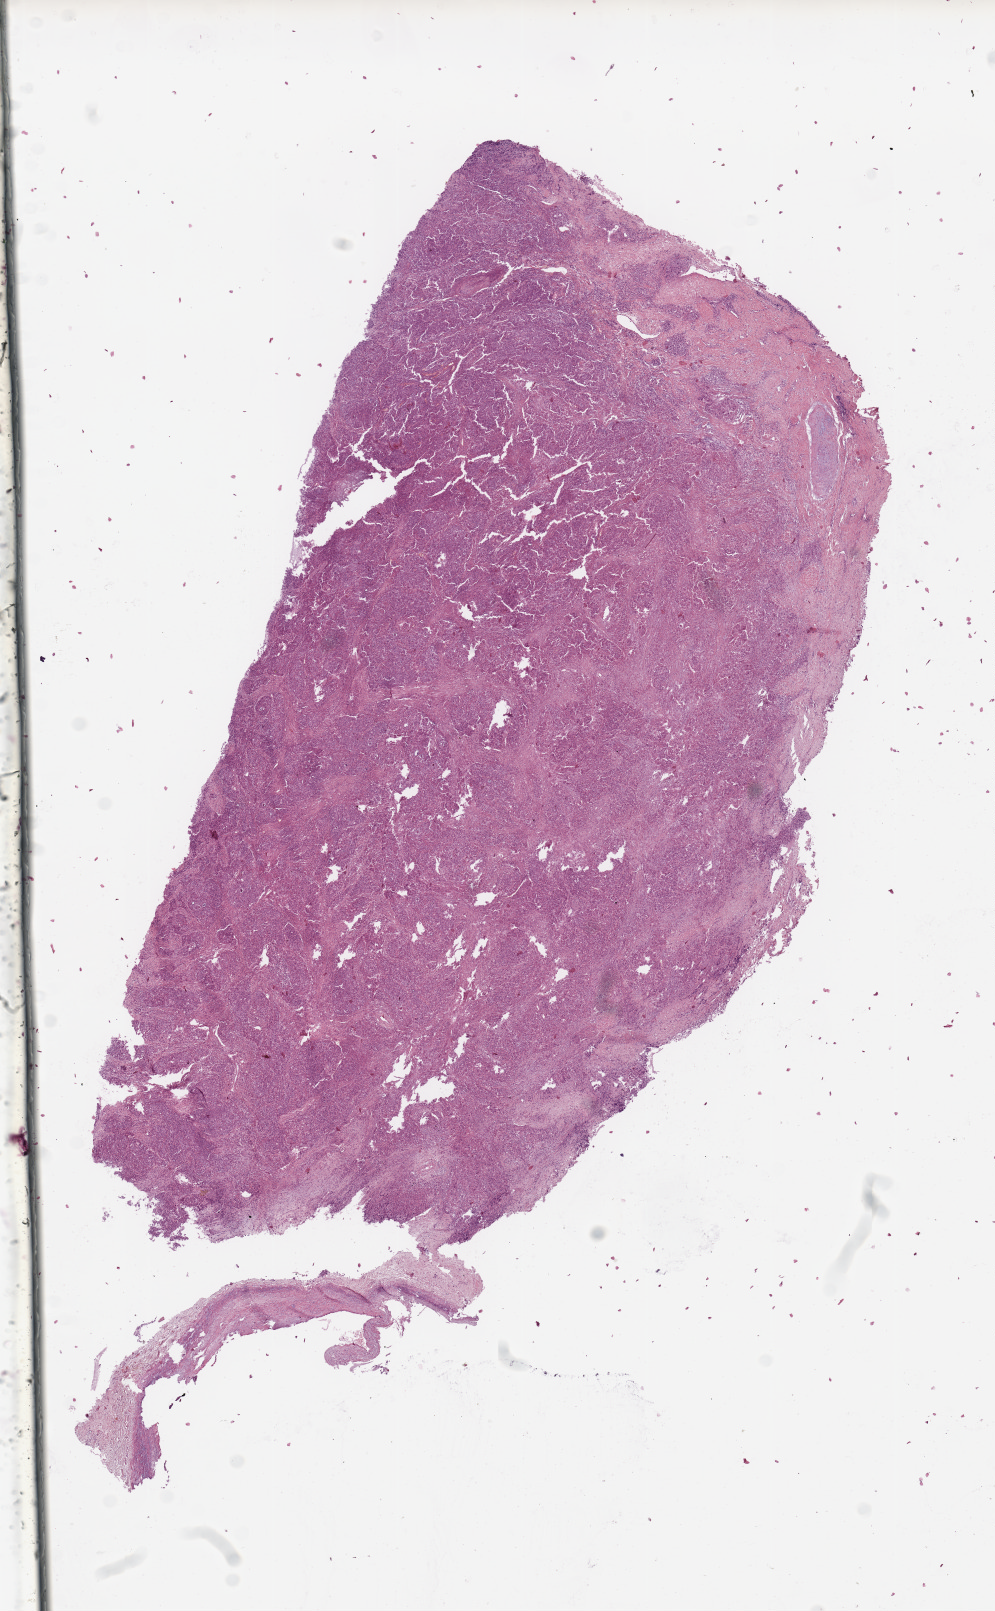
Hematoxylin and eosin (H&E) stained whole-slide image, low-resolution overview of the scanned area, about 7.9 x 12.8 mm; tumour tissue sample, lung. Patient: male, age 65 years. Histologic grade: GX (grade cannot be assessed).
AJCC pathologic stage: IA. Primary tumour site (as recorded): left upper lobe. Diagnosis: Squamous cell carcinoma, NOS.